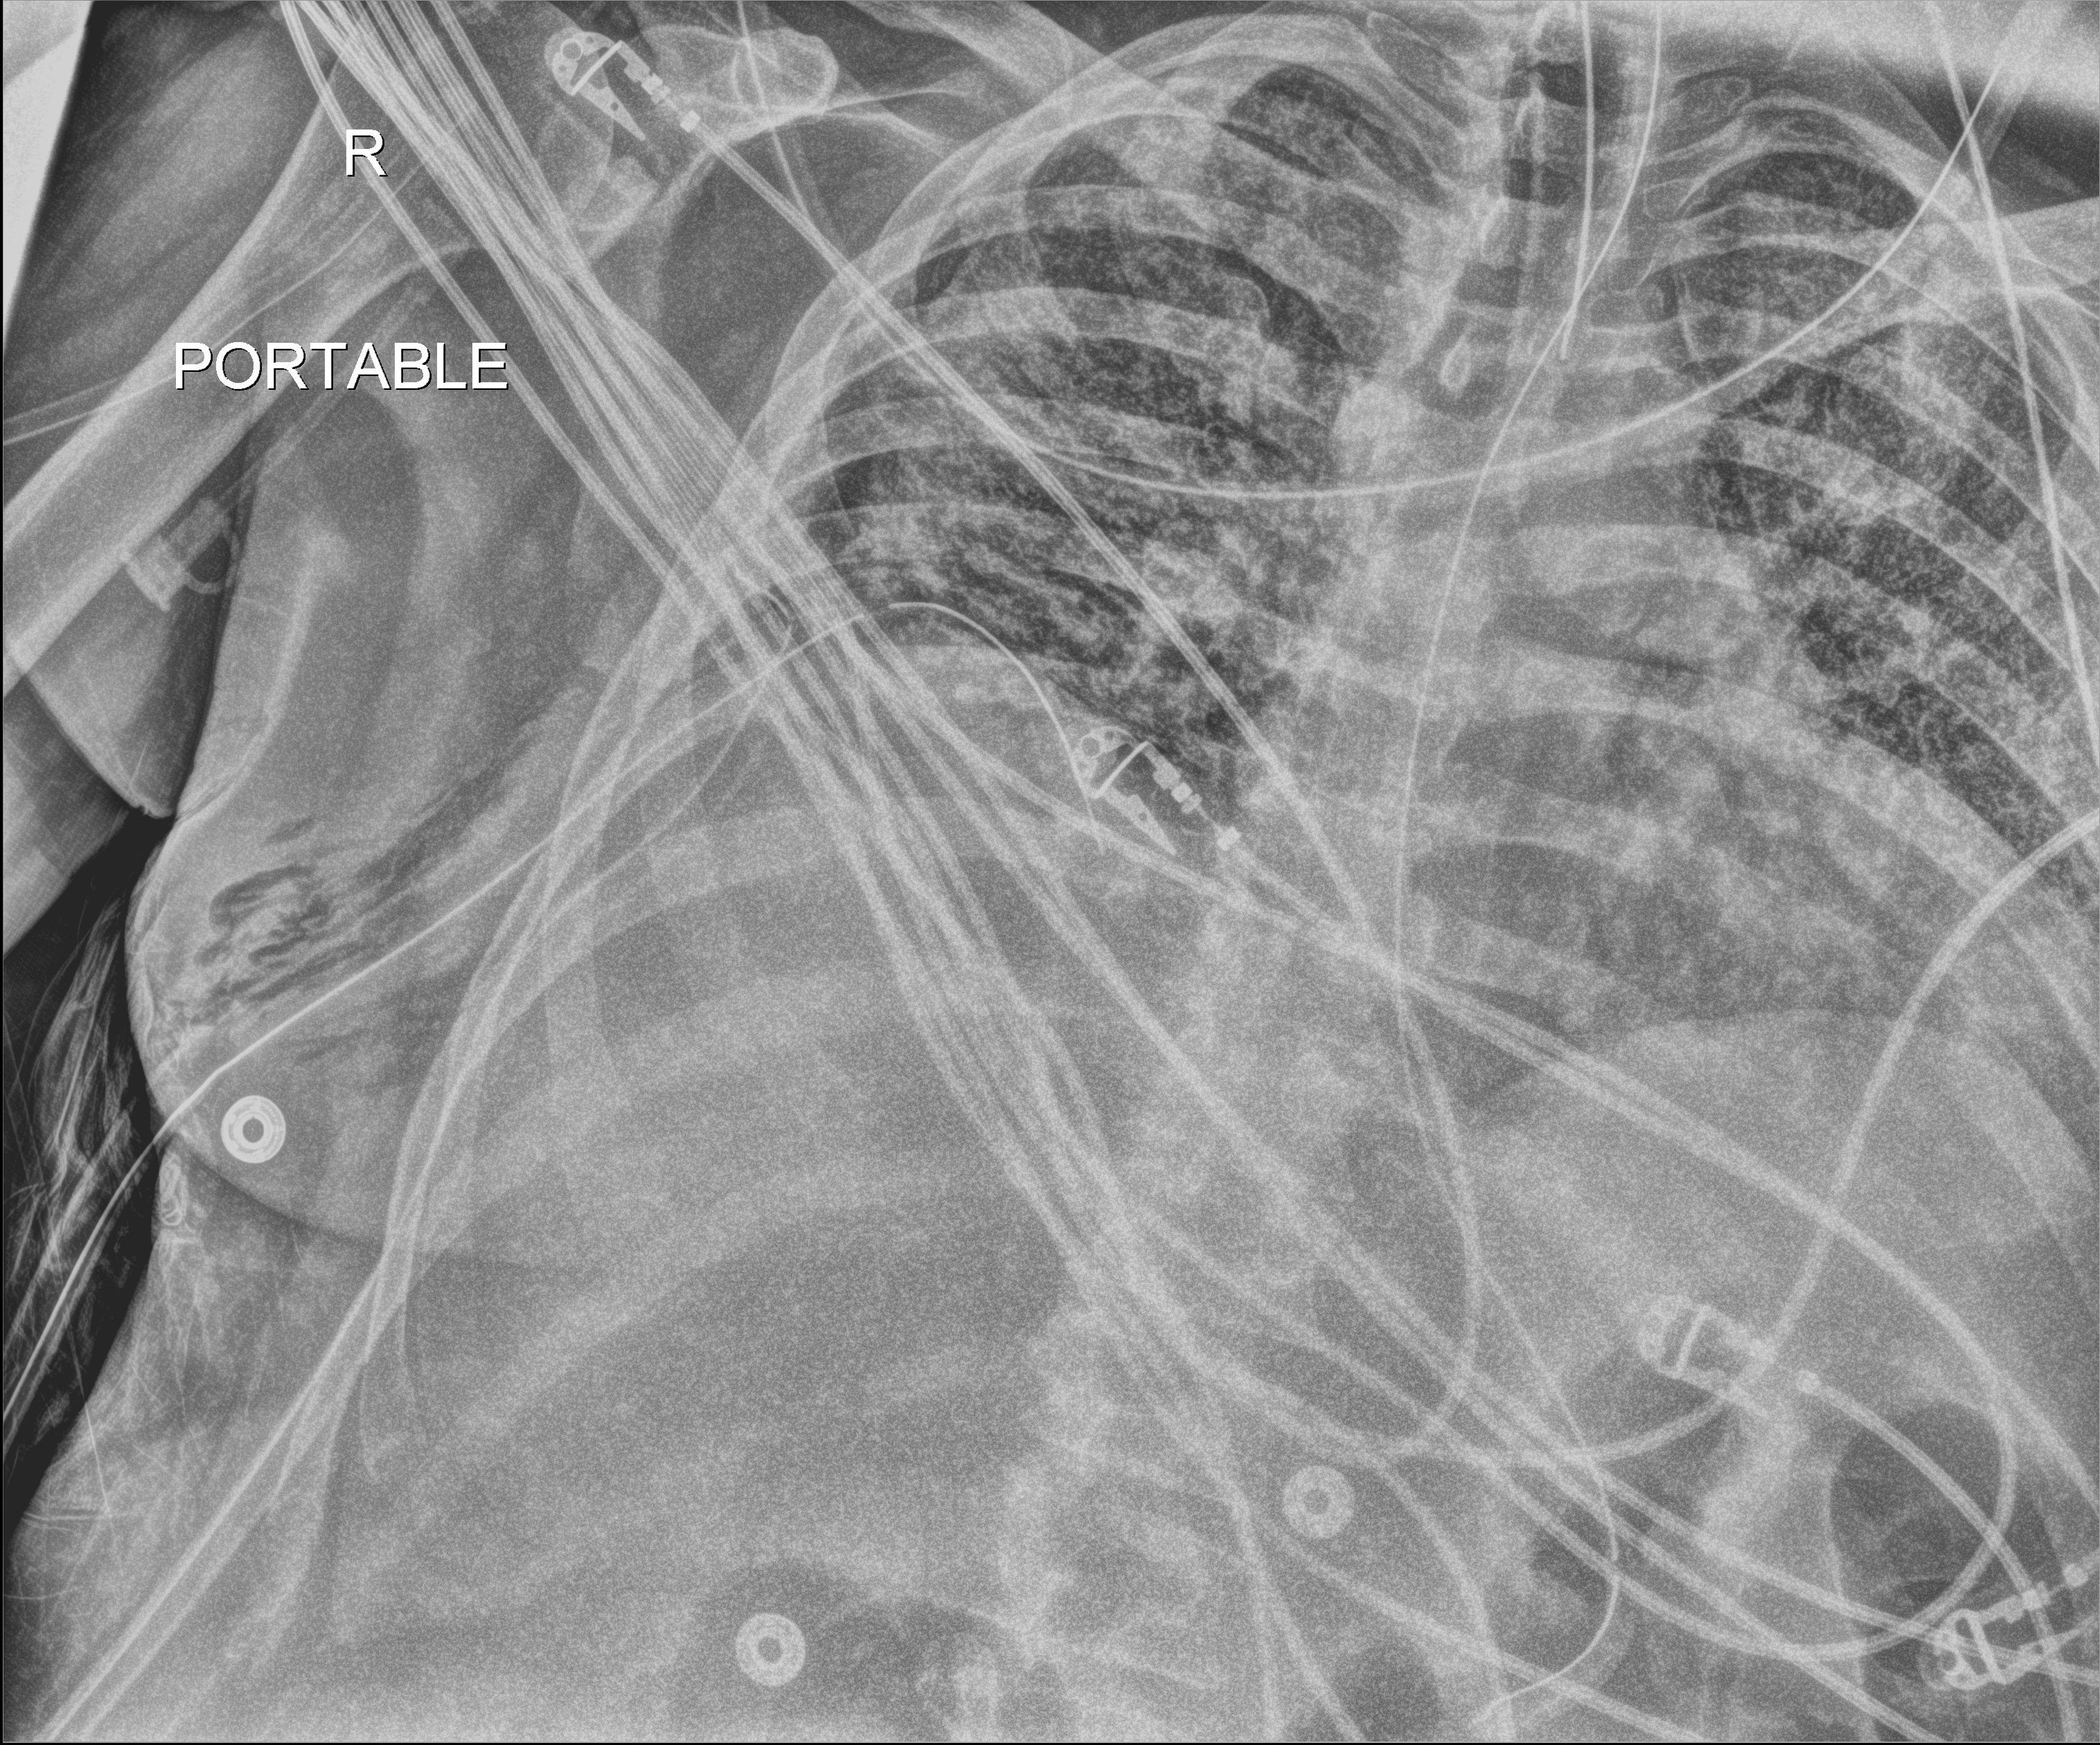
Portable chest radiograph. Male patient hospitalised with COVID-19, age 18–59 years.
From the hospital-stay record, not from the radiograph (when in the stay this image was taken is not recorded): mechanically ventilated during this hospital stay: yes.